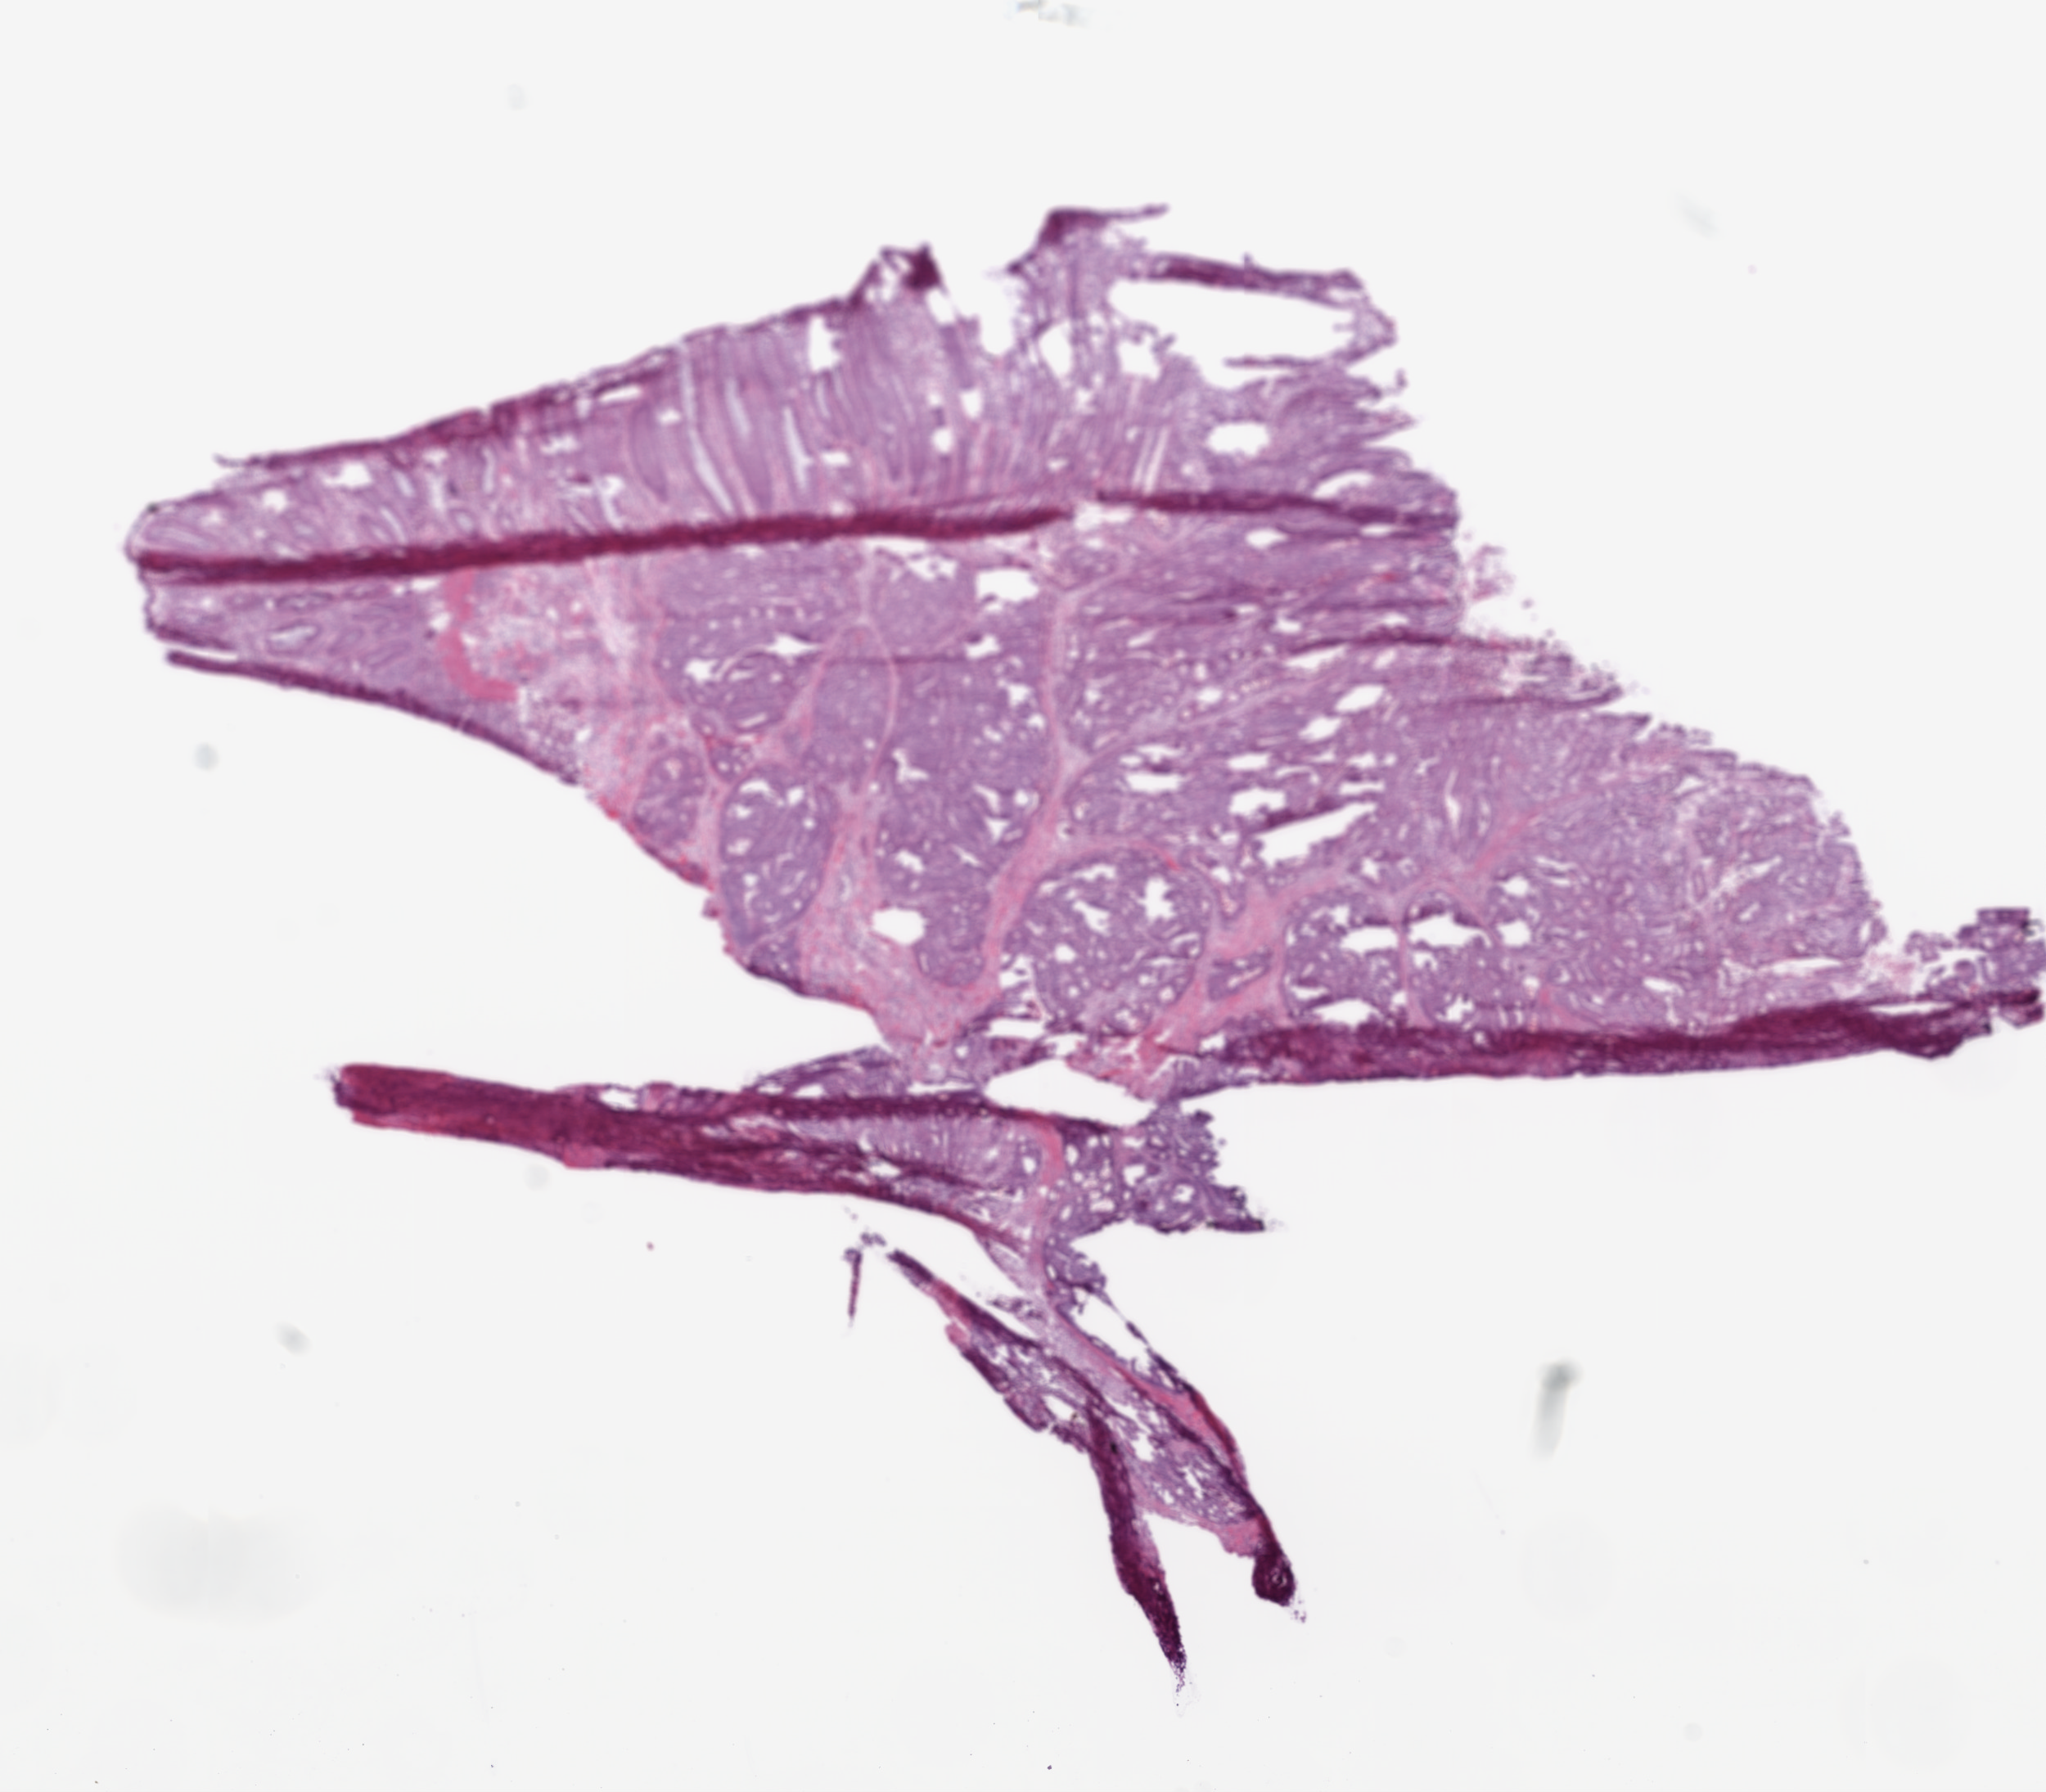
Digitized H&E-stained tissue section (whole slide) — shown as a low-resolution overview of the whole scanned area (about 10.0 x 8.8 mm, from a 20x scan); frozen section; primary tumour sample from the rectum. Male patient; age at initial diagnosis 77 years. Slide review estimates, as recorded: tumour cells 65%, tumour nuclei 70%, normal cells 25%, stromal cells 10%, necrosis 0%.
AJCC pathologic stage: IVA (7th edition). Histologic diagnosis: Adenocarcinoma, NOS.